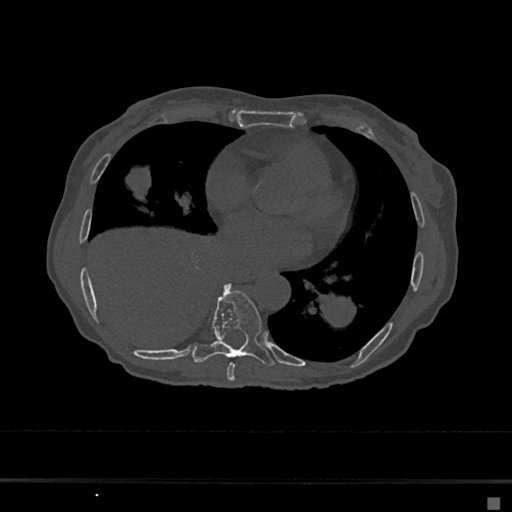
CT including the spine, one axial slice; position 330 of 797 along the scan axis; 120 kVp; bone window (W 1800 / L 400 HU); 0.5 mm slice thickness; 512 × 512 image matrix, field of view 360 × 360 mm. Female patient, age 68 years. From the clinical record (not read from this slice): primary cancer: renal.
Annotated regions visible in this slice (semi-automatically segmented with operator editing):
- T7 vertebra: box from (x=227, y=363) to (x=235, y=381) px
- T8 vertebra: (x=192, y=284)–(x=274, y=366)